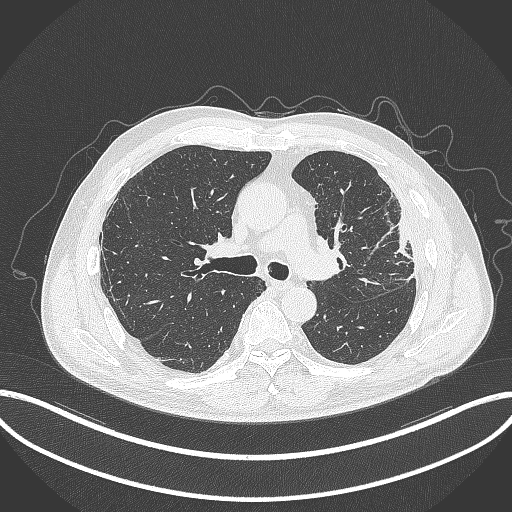
Chest CT, one axial slice; slice 214 of 382 in the series (ordered by position); lung window (W 1500 / L -600 HU); 1 mm slice thickness; 512 × 512 image matrix. Male patient, age 64 years. Case-level facts recorded for this patient, not image findings: clinical TNM (as recorded): T4 N1 M0.
Outlined on this slice (bounding box drawn by a radiologist):
- lung tumour (recorded histology: adenocarcinoma): box from (x=387, y=209) to (x=416, y=263) px